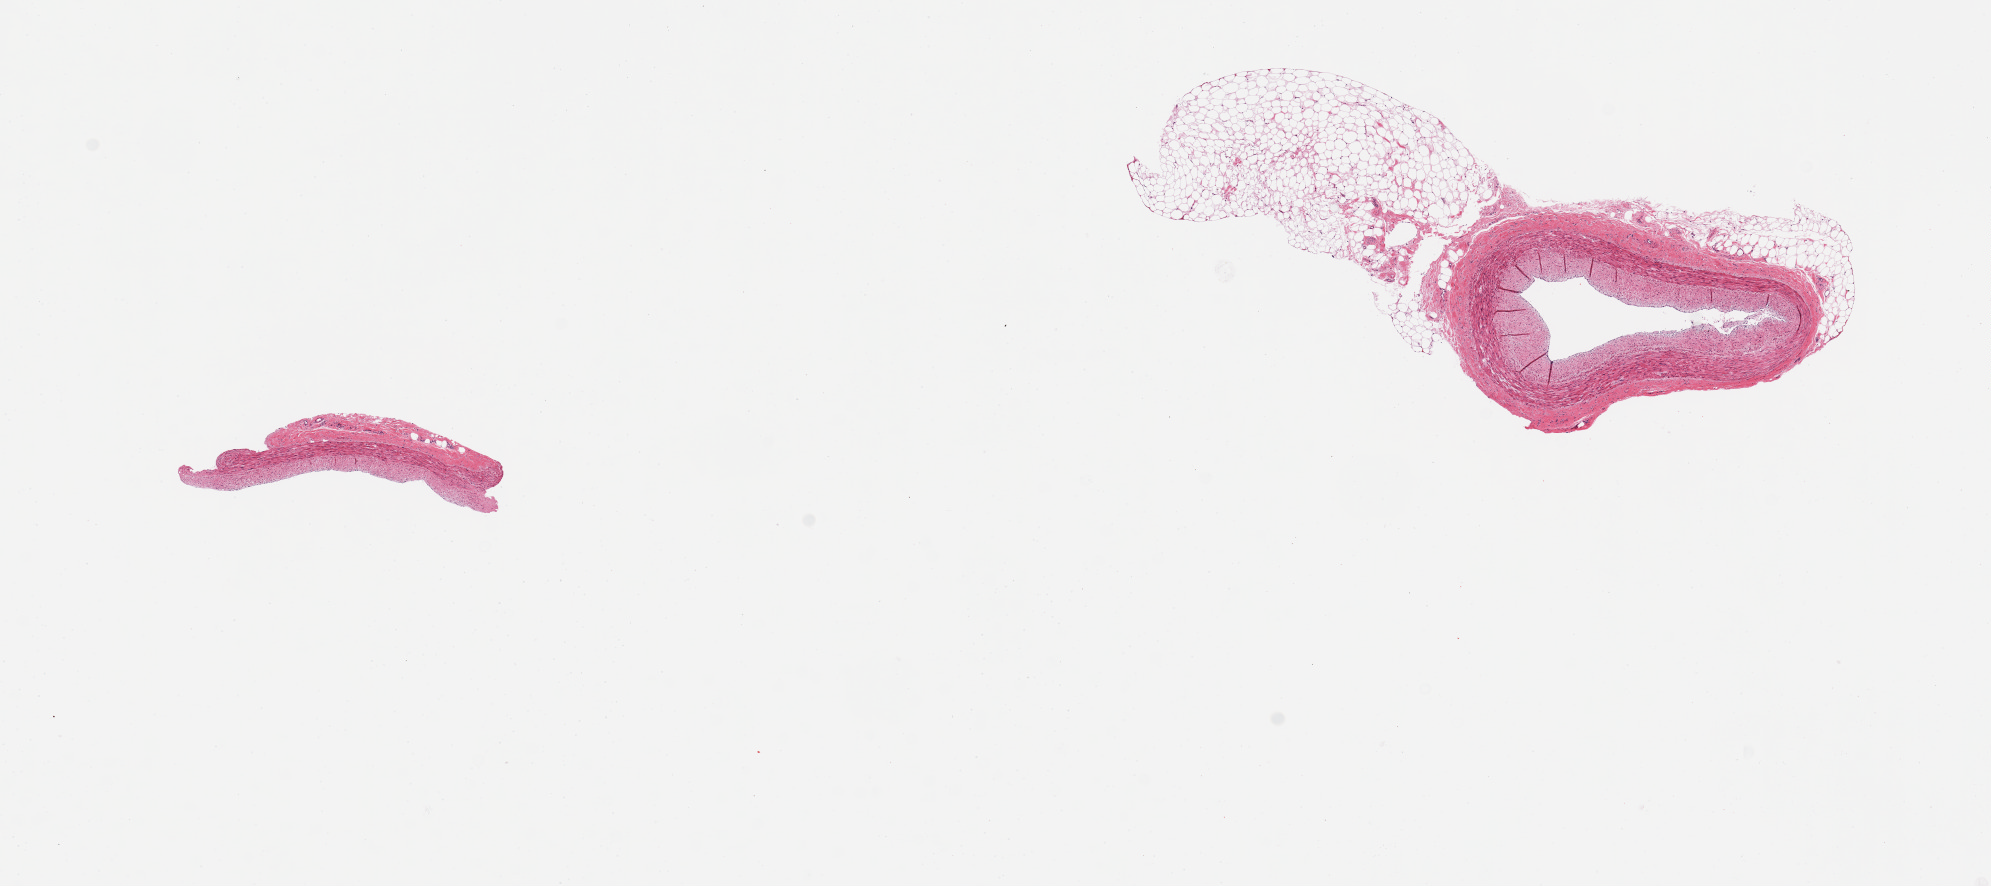
Digitized H&E-stained section, brightfield — shown as a low-resolution overview of the whole scanned area (about 15.8 x 7.0 mm), PAXgene-fixed, paraffin-embedded tissue, sampled site (target tissue): coronary artery, donor tissue sample. Donor sex: female.
Pathologist's review note for this sample: 2 pieces, minimal atherosis; one is fragment of vessel wall; the other is complete, adherent nubbins of fat, up to ~2mm.